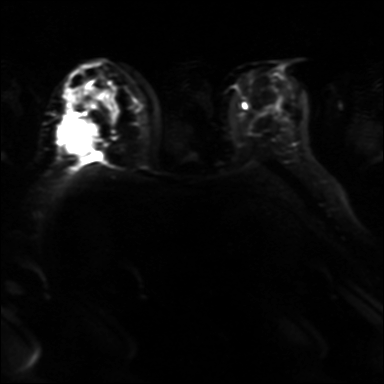
Breast MRI, one axial slice; slice 19 of 36 in the series (ordered by position); diffusion-weighted series; image 2 of 4 stored at this slice position (different b-values; order by instance number); 3 T; 384 × 384 image matrix. Female patient.
Structures marked on this image (outlined manually by an expert reader):
- tumour on diffusion-weighted imaging: bounding box <58,120,98,154> (left, top, right, bottom; pixels)